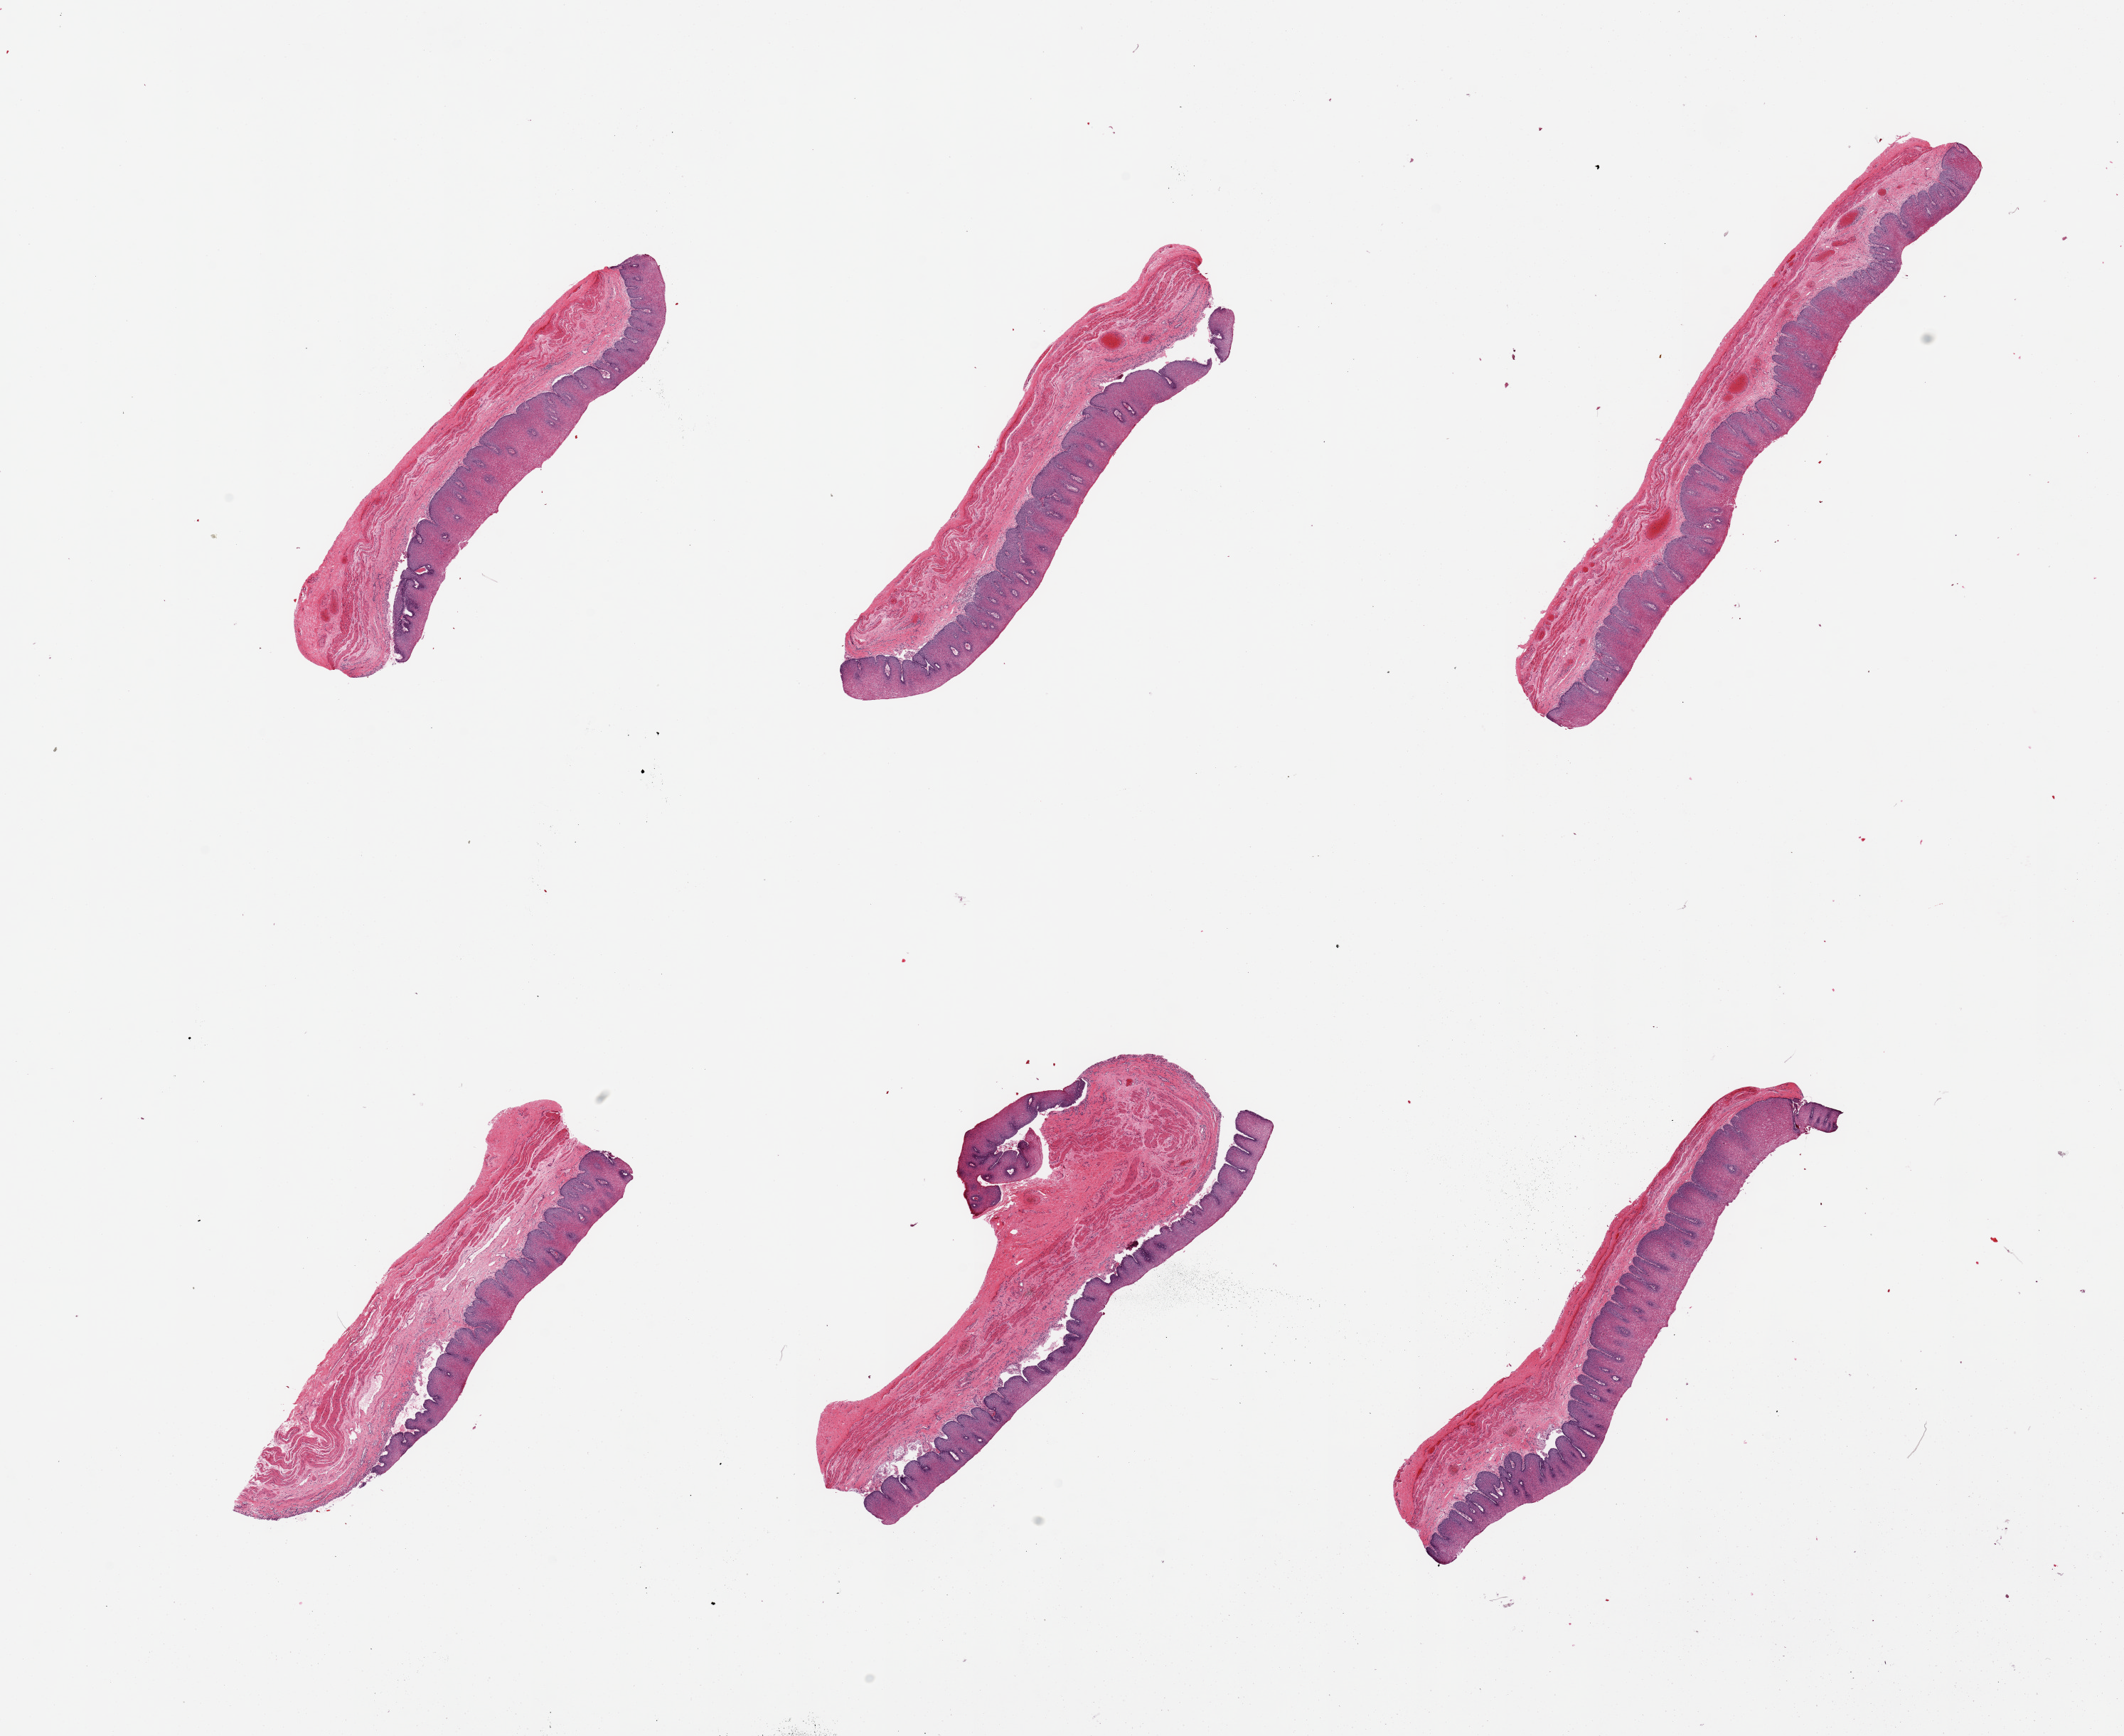
Digitized H&E-stained section, brightfield — whole scanned area (about 23.6 x 19.3 mm, from a 20x scan) shown as a low-resolution overview. PAXgene-fixed, paraffin-embedded tissue. Sampled site (target tissue): esophageal mucous membrane. Tissue donor sample.
Pathologist's review note for this sample: 6 pieces, prominent squamous hyperplasia up to ~50% thickness.